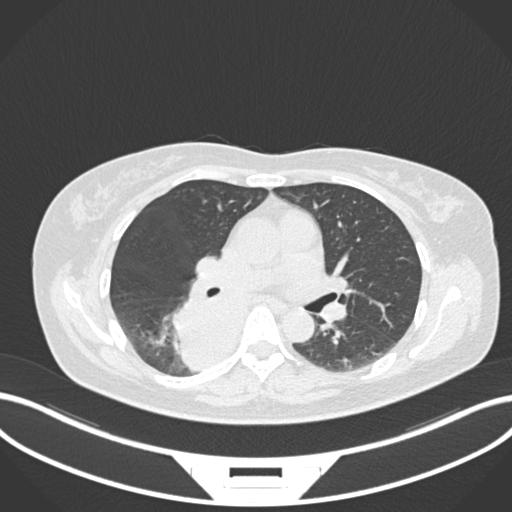
Chest CT, one axial slice; reconstruction kernel B30f; lung window (W 1500 / L -600 HU); 1 mm slice thickness; 512 × 512 image matrix, field of view 400 × 400 mm. Female patient, age 54 years. From the clinical record (not read from this slice): clinical TNM (as recorded): T4 N0 M0.
Structures marked on this image (bounding box drawn by a radiologist):
- lung tumour (recorded histology: adenocarcinoma): bounding box (x1, y1, x2, y2) in pixels: (170, 287, 256, 378)